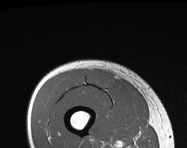
MRI of an extremity soft-tissue mass, one axial slice. Position 37 of 114 along the scan axis. MR volume resampled by the dataset authors to the PET/CT grid (not the native acquisition matrix). 3.27 mm slice thickness. 187 × 148 image matrix, field of view 183 × 145 mm. Male patient. Case-level facts recorded for this patient, not image findings: histological type: pleiomorphic leiomyosarcoma; grade: intermediate; site of the primary tumour: right thigh.
Annotated regions visible in this slice (expert contour drawn on MRI and transferred to this co-registered scan by the dataset authors):
- gross tumour volume including surrounding oedema: bounding box <88,70,113,87> (left, top, right, bottom; pixels)